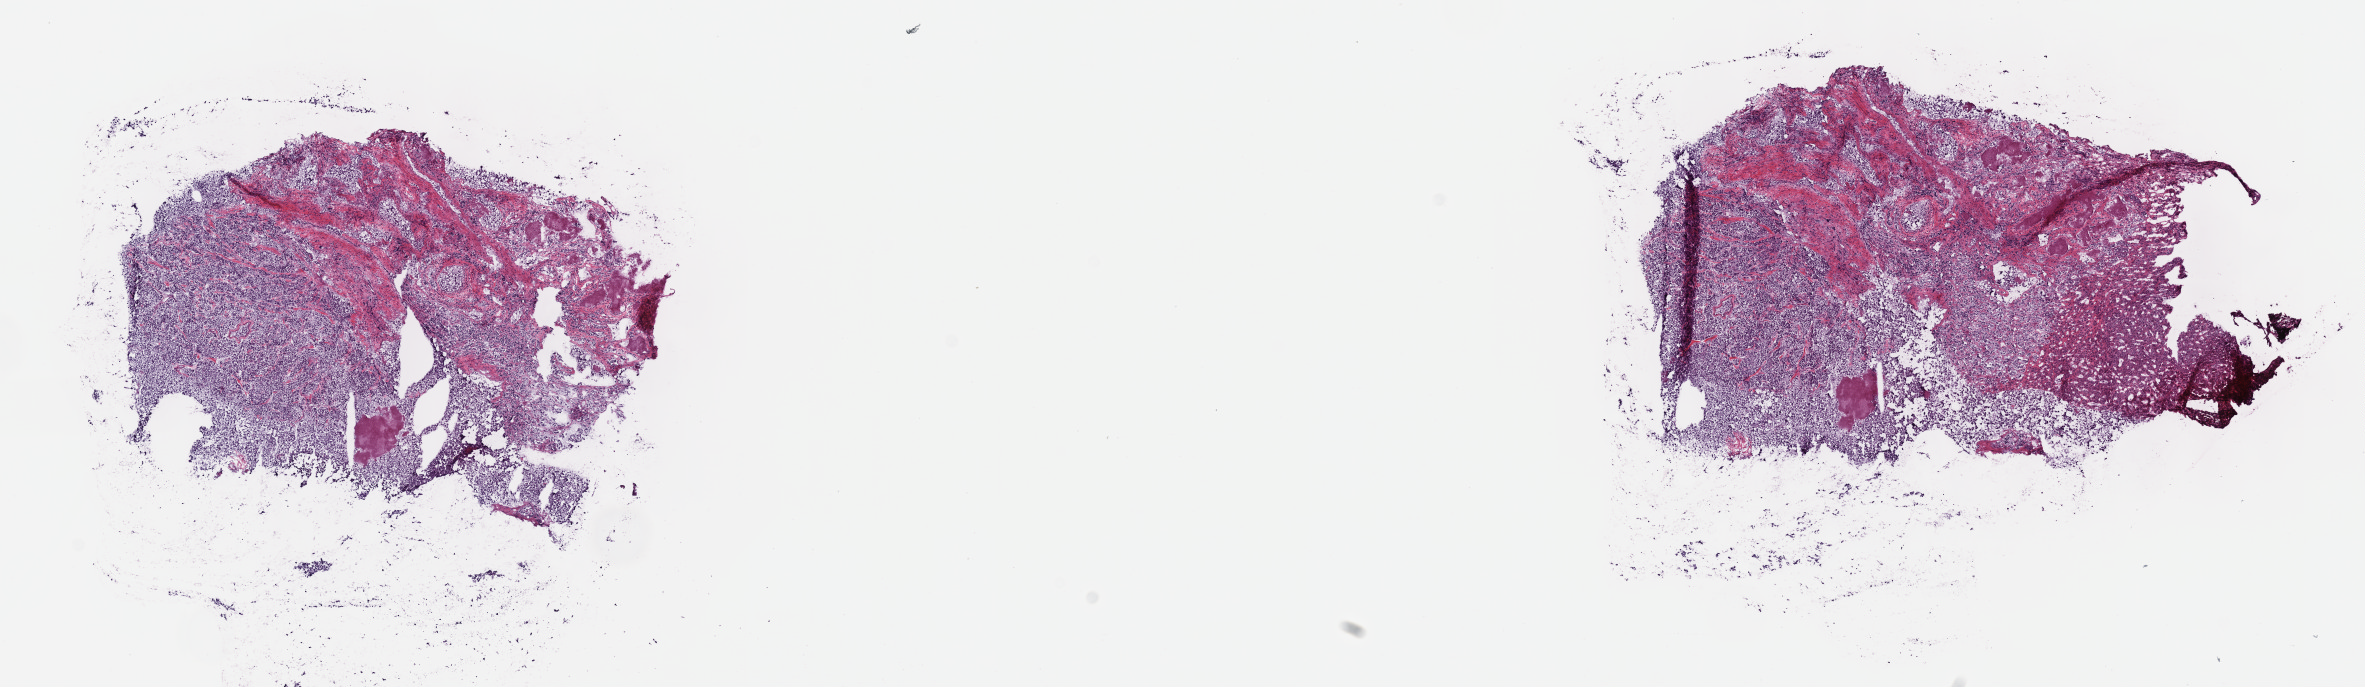
Whole-slide histology image, Hematoxylin and eosin (H&E) stained — whole scanned area (about 19.1 x 5.6 mm) shown as a low-resolution overview, frozen section, adrenal gland, primary tumour sample. Male patient; age at initial diagnosis 27 years. Slide review estimates, as recorded: tumour cells 70%, tumour nuclei 70%.
Histologic diagnosis: Pheochromocytoma, NOS.